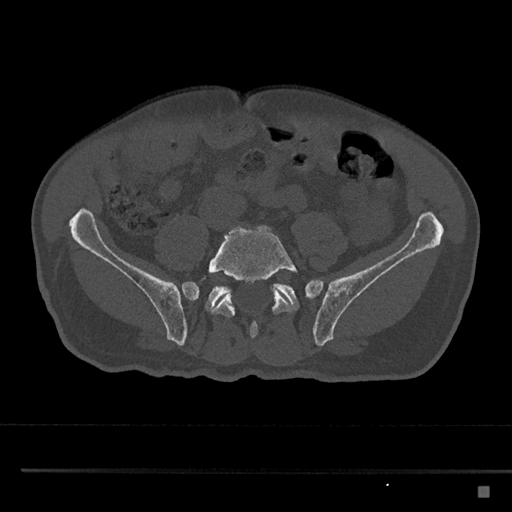
CT including the spine, one axial slice; slice 569 of 797 in the series (ordered by position); reconstruction kernel Br40s/3; 120 kVp; bone window (W 1800 / L 400 HU); 512 × 512 image matrix, field of view 391 × 391 mm. Patient: male, 59 years. From the clinical record (not read from this slice): primary cancer: prostate.
Annotated regions visible in this slice (semi-automatically segmented with operator editing):
- L5 vertebra: box from (x=208, y=225) to (x=297, y=338) px